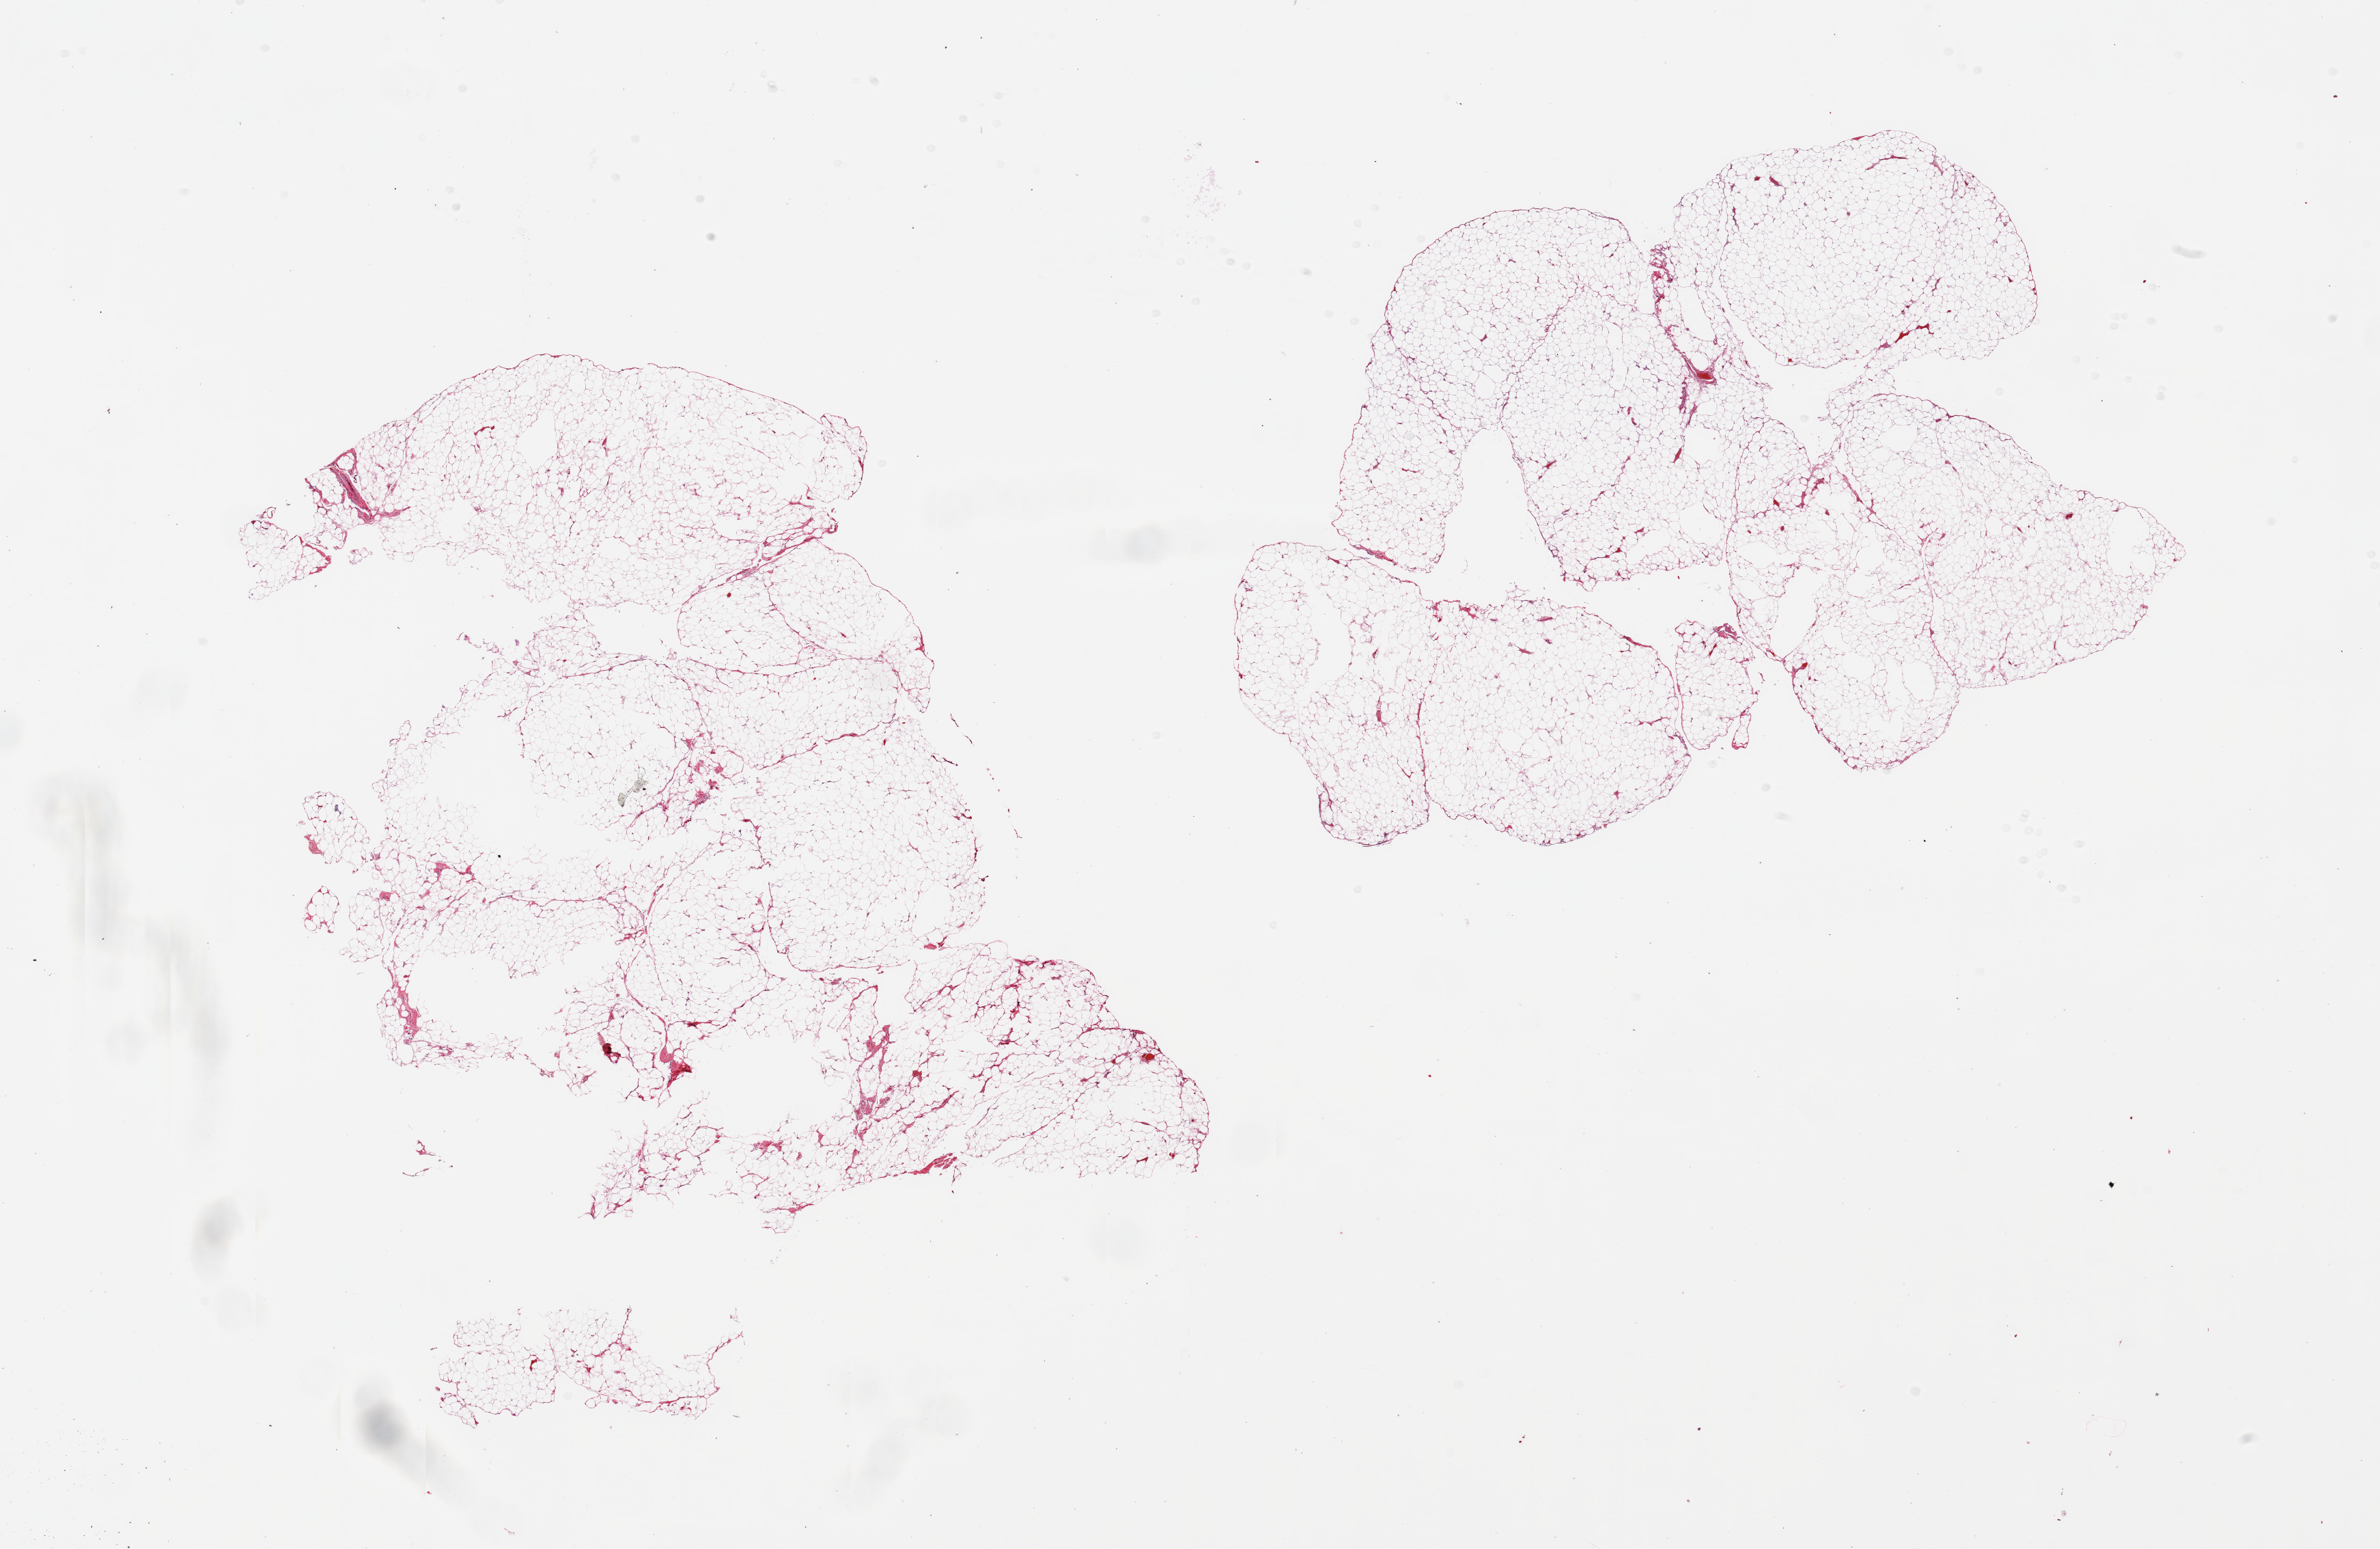
Whole-slide image, H&E stain, a low-resolution overview of the entire scanned area, about 27.6 x 17.9 mm (slide scanned at 20x), PAXgene-fixed, paraffin-embedded tissue, target tissue: omentum, donor tissue sample. Male donor.
Reviewer comment on this tissue sample: 2 pieces; lobulated mature adipose tissue with septal vessels.